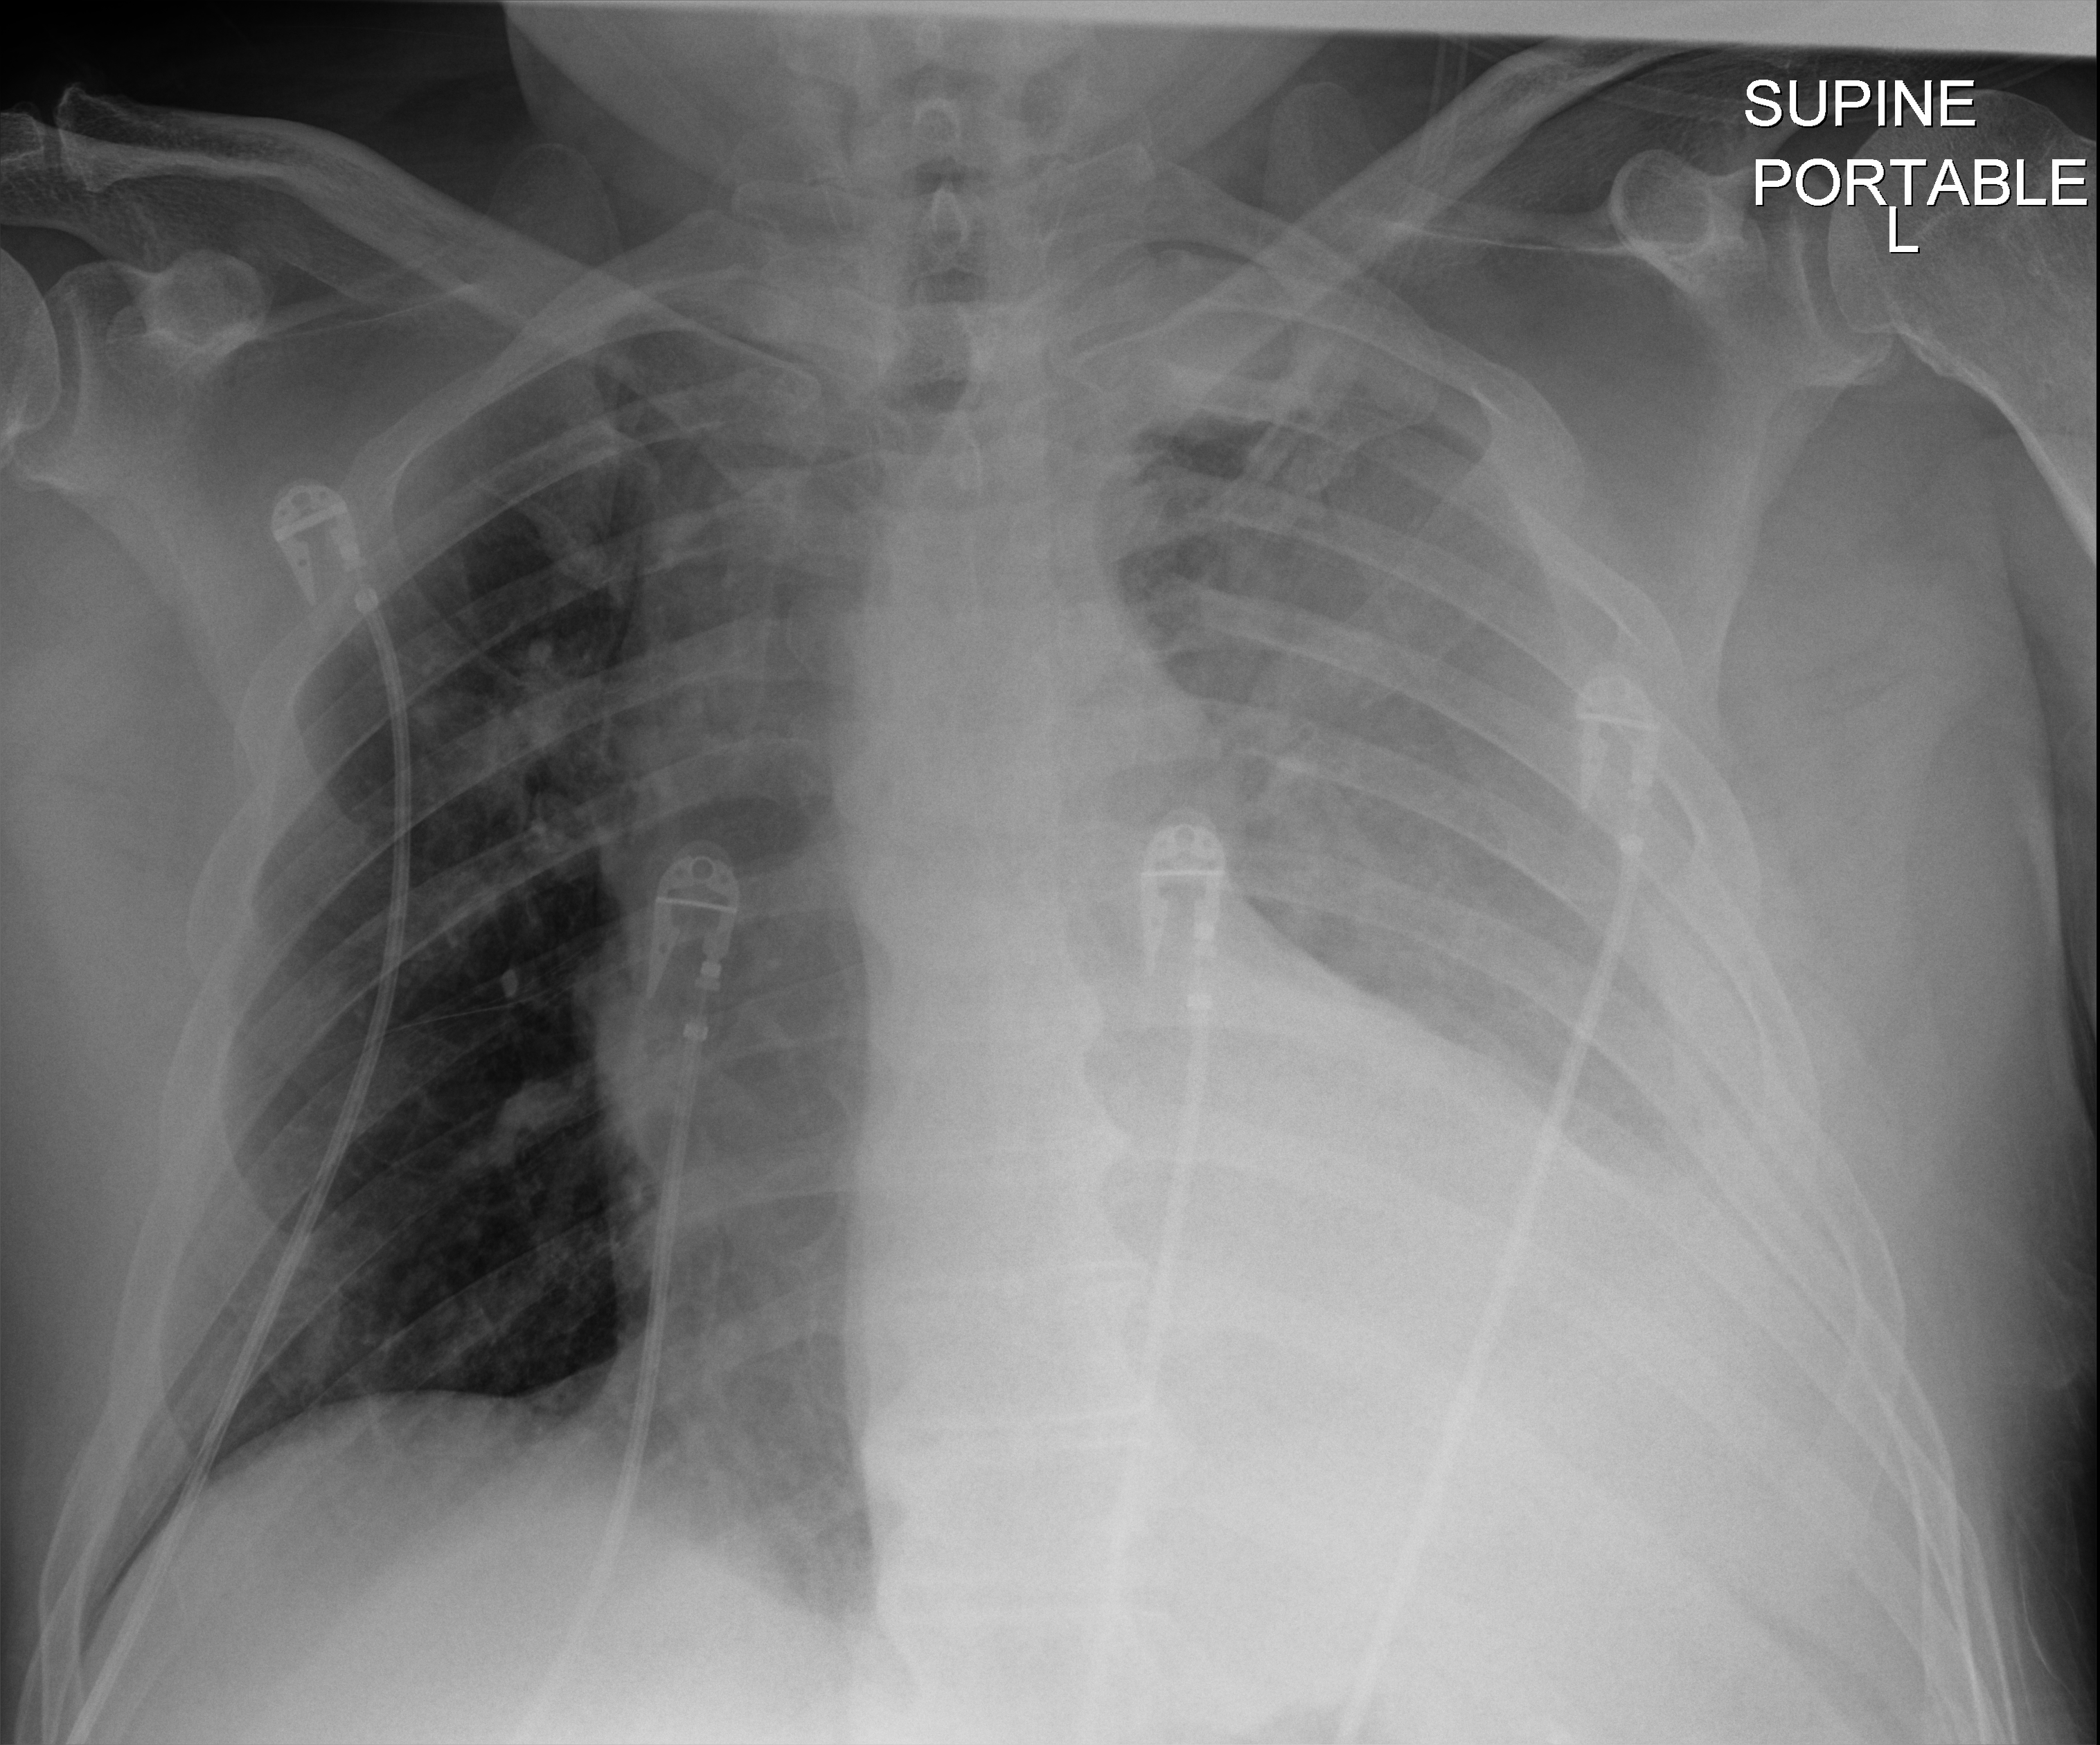
Chest X-ray (portable); anteroposterior (AP) projection. Patient hospitalised with COVID-19; male, aged 18–59 years.
Hospital-stay facts (about this admission, not read from this image; timing relative to this image not recorded): length of hospital stay: 10 days; admitted to intensive care during this hospital stay: no.